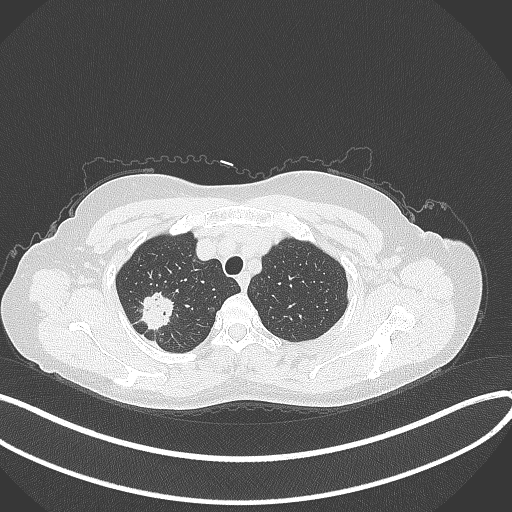
Chest CT, one axial slice; slice 306 of 337 in the series (ordered by position); lung window (W 1500 / L -600 HU); 1 mm slice thickness; 512 × 512 image matrix, field of view 400 × 400 mm. Female patient, age 50 years. From the clinical record (not read from this slice): clinical TNM (as recorded): T1c N0 M0.
Outlined on this slice (rectangle marked by the reading radiologist):
- lung tumour (recorded histology: adenocarcinoma): box from (x=137, y=285) to (x=176, y=331) px